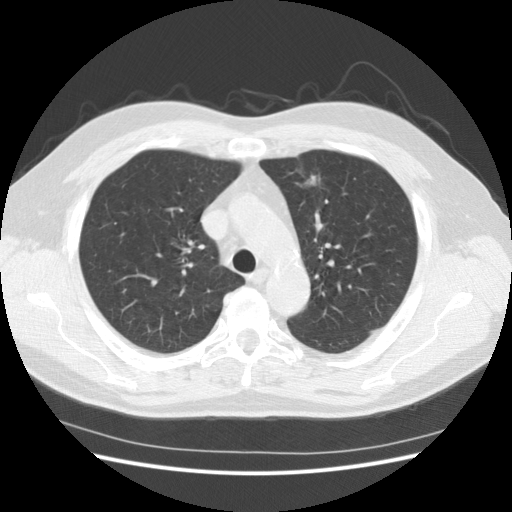
Low-dose screening chest CT, axial slice. Baseline screening round. Lung window (W 1500 / L -600 HU). 2.5 mm slice thickness. Slice 44 of 151 in the series. 512 × 512 image matrix. Male participant, aged 63 years at enrolment.
Expert reader's lesion annotation, box from (x=282, y=153) to (x=337, y=205) px. The exam's reader record, not a measurement of the box and not confirmed to be the same lesion: non-calcified nodule or mass ≥4 mm, lingula, 18 × 9 mm, poorly defined margins, soft tissue attenuation. Participant outcome: lung cancer diagnosed 475 days after this screen (after the second annual screen) — adenocarcinoma, NOS, left upper lobe, moderately differentiated (G2), stage IA (AJCC 6th edition), 14 mm at pathology.